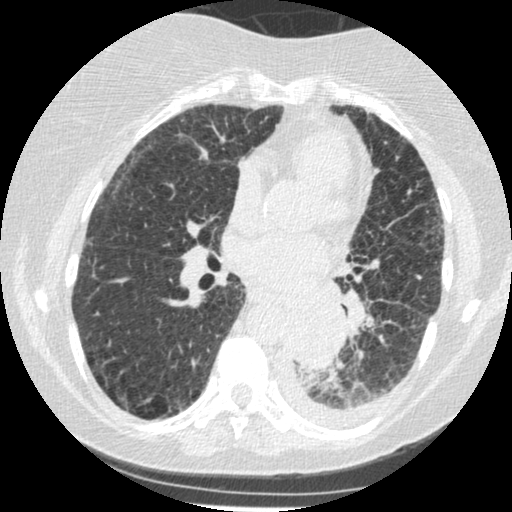
Axial slice from a low-dose chest CT screening exam. Third screening round (two years after baseline). Lung window (W 1500 / L -600 HU). Slice 225 of 341 in the series. 512 × 512 image matrix. Female participant, aged 60 years at enrolment. Former smoker at enrolment.
• Lesion marked by an expert reader, bounding box (x1, y1, x2, y2) in pixels: (274, 304, 342, 375).
• The exam's reader record, not a measurement of the box and not confirmed to be the same lesion: non-calcified nodule or mass ≥4 mm, left lower lobe, 54 × 38 mm, smooth margins, soft tissue attenuation, pre-existing on the prior screen: yes; interval growth: yes.
• Official screen result: positive, other.
• Lung cancer was diagnosed 15 days after this screen: small cell carcinoma, NOS, left lower lobe, undifferentiated (G4), stage IV (AJCC 6th edition), 69 mm at pathology.